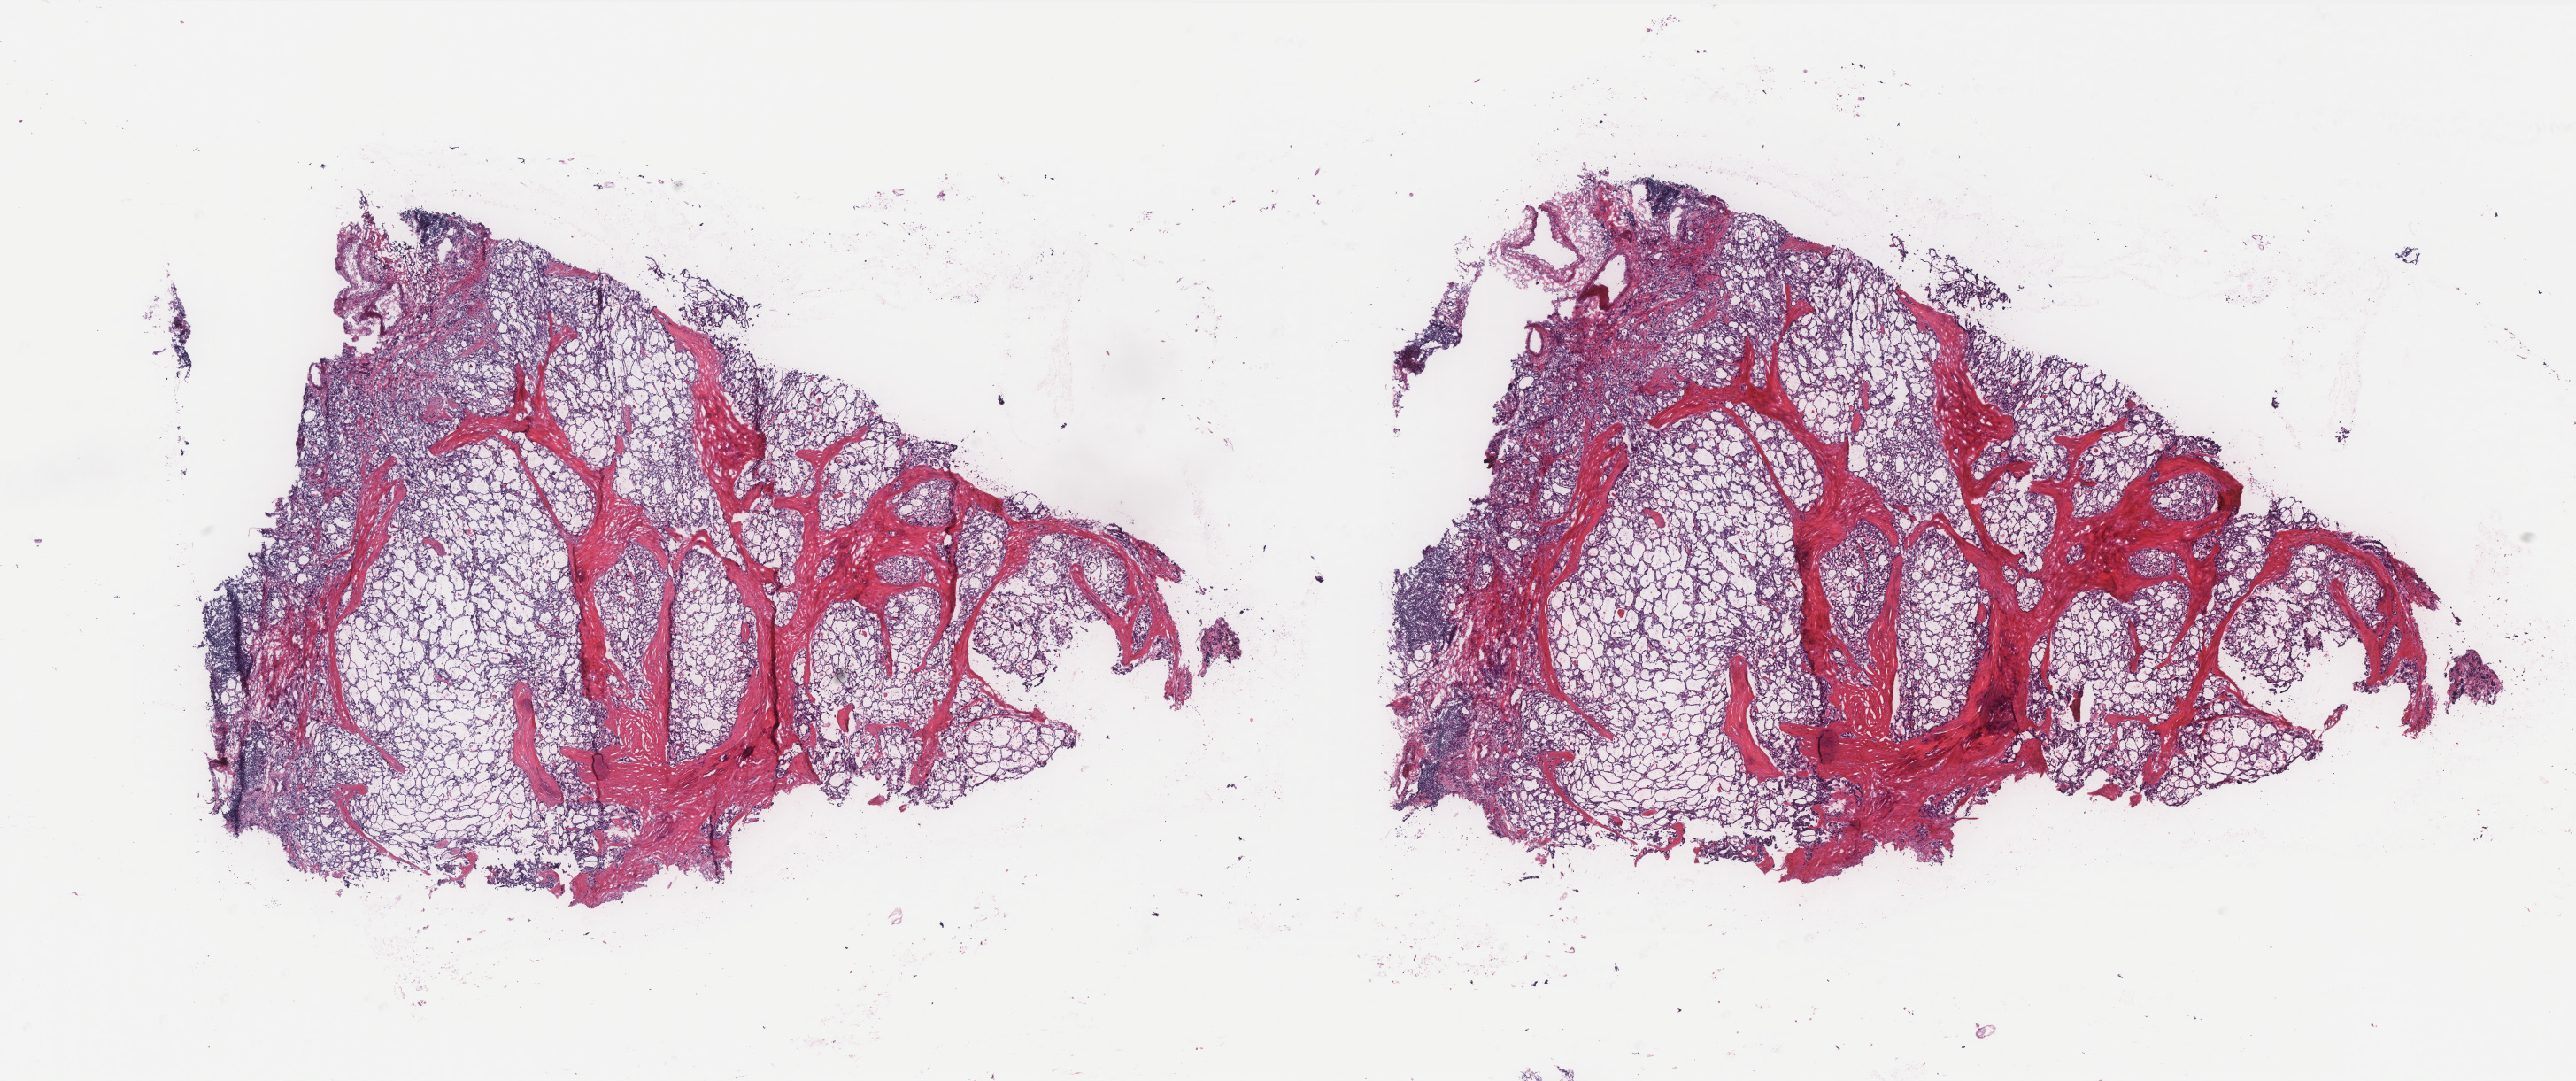
Hematoxylin and eosin (H&E) stained whole-slide image, low-resolution overview of the scanned area, about 23.3 x 9.8 mm (slide scanned at 40x); frozen section from the bottom of the tissue portion; thyroid, primary tumour sample. Female patient; age at initial diagnosis 33 years. Pathologist review of this section (percent, as recorded): tumour cells 0%, tumour nuclei 0%, normal cells 65%, stromal cells 35%, necrosis 0%. Inflammatory infiltration, as recorded: lymphocyte infiltration 0%, monocyte infiltration 0%, neutrophil infiltration 0%.
Laterality: left. Lymph nodes positive (case pathology): 0 of 3 examined. Pathologic diagnosis: Papillary adenocarcinoma, NOS (thyroid gland). AJCC pathologic stage: I.